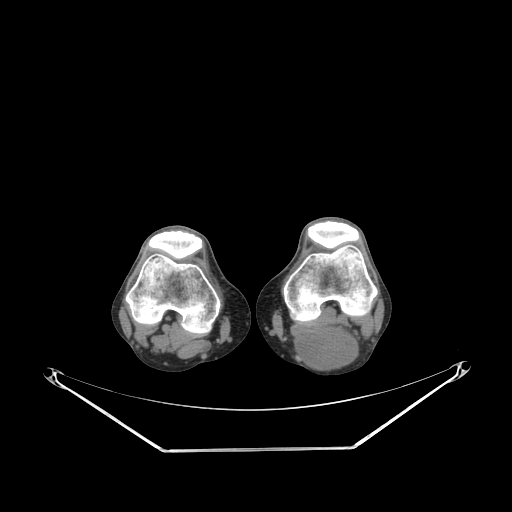
CT of an extremity soft-tissue mass (from a PET/CT study), one axial slice. Position 180 of 267 along the scan axis. 140 kVp. Soft-tissue window (W 400 / L 40 HU). 3.75 mm slice thickness. 512 × 512 image matrix, field of view 500 × 500 mm. Male patient. From the clinical record (not read from this slice): histological type: synovial sarcoma; site of the primary tumour: left poplietal fossa.
Outlined on this slice (expert contour drawn on MRI and transferred to this co-registered scan by the dataset authors):
- gross tumour volume (mass): box from (x=292, y=327) to (x=359, y=369) px